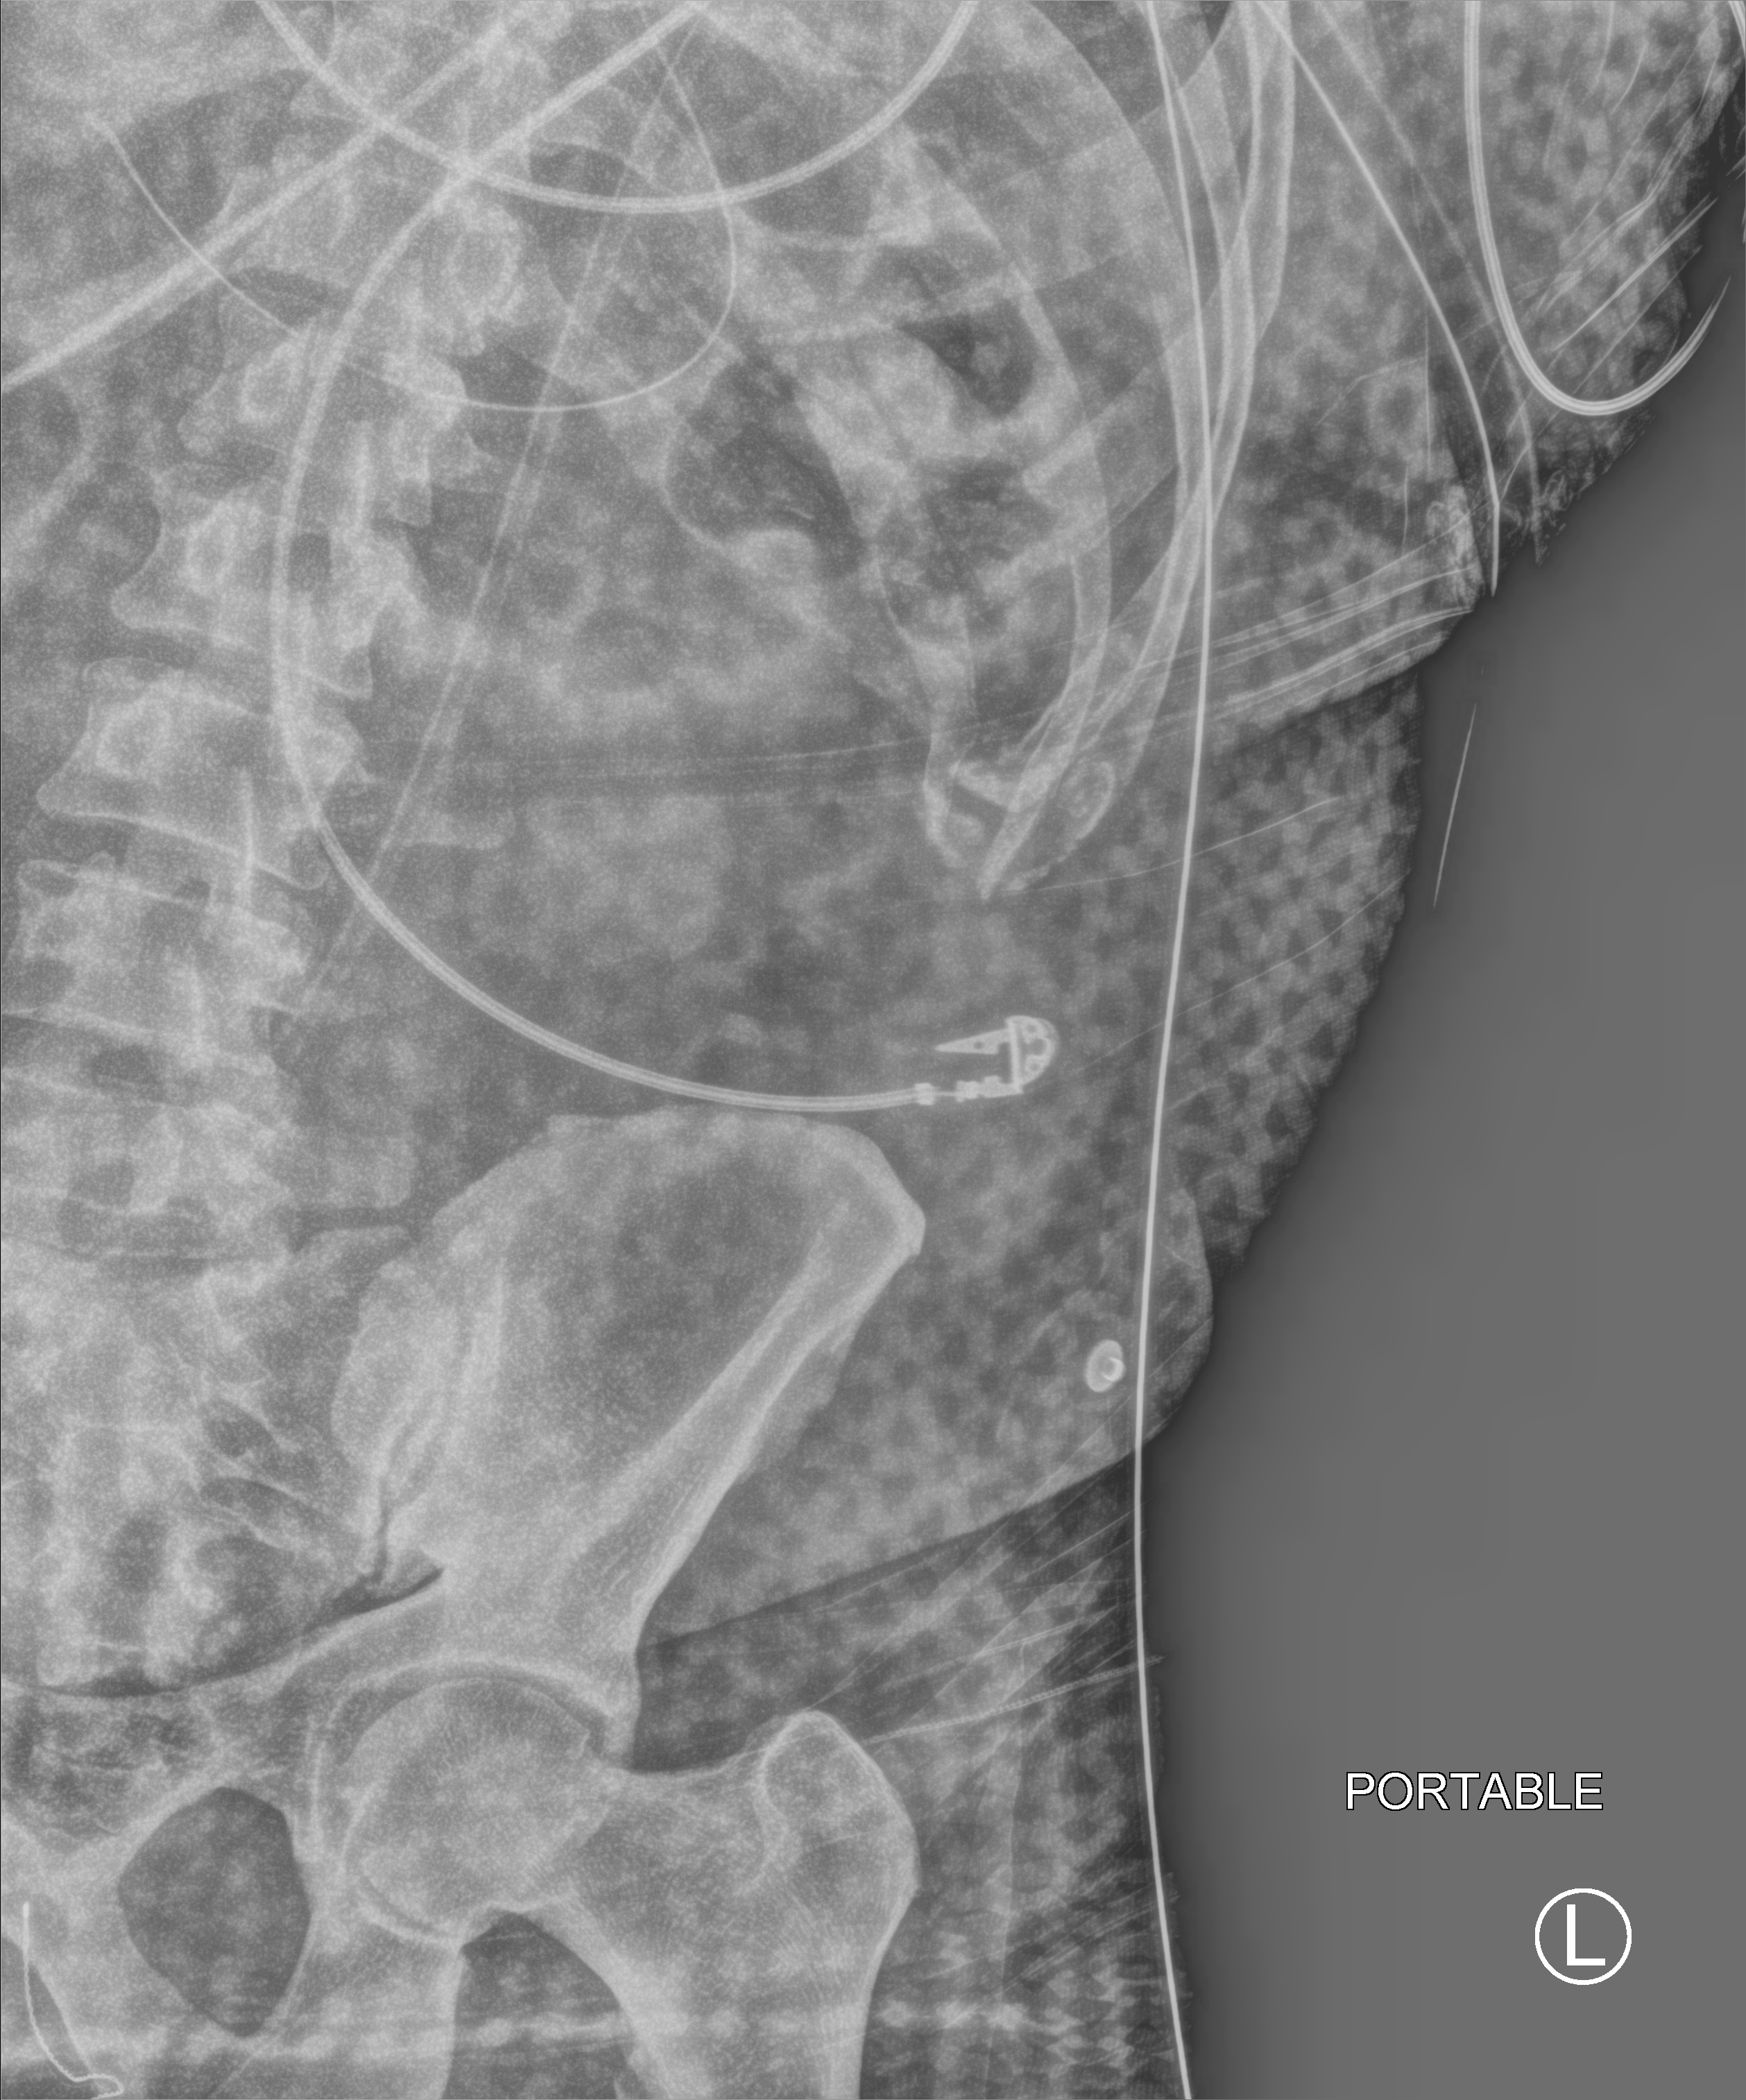
Bedside abdomen radiograph (computed radiography). Male patient hospitalised with COVID-19, age 18–59 years.
From the hospital-stay record, not from the radiograph (when in the stay this image was taken is not recorded): length of hospital stay: 29 days; admitted to intensive care during this hospital stay: yes; mechanically ventilated during this hospital stay: yes.